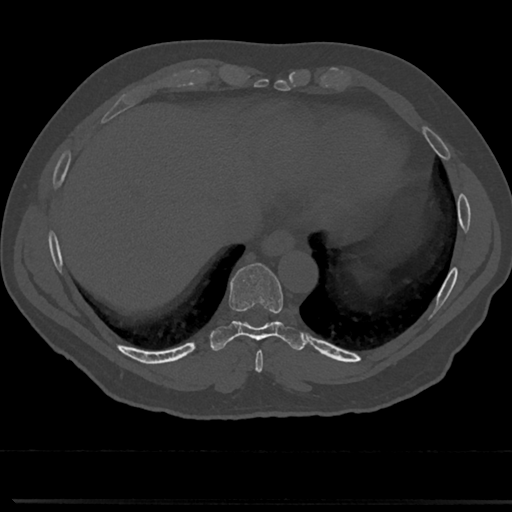
CT including the spine, one axial slice; slice 306 of 817 in the series (ordered by position); reconstruction kernel Br40s/3; 120 kVp; bone window (W 1800 / L 400 HU); 0.5 mm slice thickness; 512 × 512 image matrix. Patient: male, 61 years. Case-level facts recorded for this patient, not image findings: primary cancer: prostate.
Outlined on this slice (semi-automatic segmentation, software-assisted and operator-edited):
- T8 vertebra: box from (x=232, y=304) to (x=287, y=355) px
- T9 vertebra: (x=232, y=266)–(x=283, y=329)